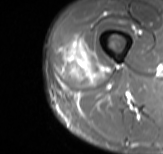
MRI of an extremity soft-tissue mass, one axial slice; slice 19 of 61 in the series (ordered by position); STIR; MR volume resampled by the dataset authors to the PET/CT grid (not the native acquisition matrix); 3.27 mm slice thickness; 163 × 154 image matrix. Male patient. From the clinical record (not read from this slice): histological type: poorly differentiated synovial sarcoma; grade: high; site of the primary tumour: right buttock.
Structures marked on this image (expert contour drawn on MRI and transferred to this co-registered scan by the dataset authors):
- gross tumour volume including surrounding oedema: bounding box (x1, y1, x2, y2) in pixels: (62, 39, 108, 83)